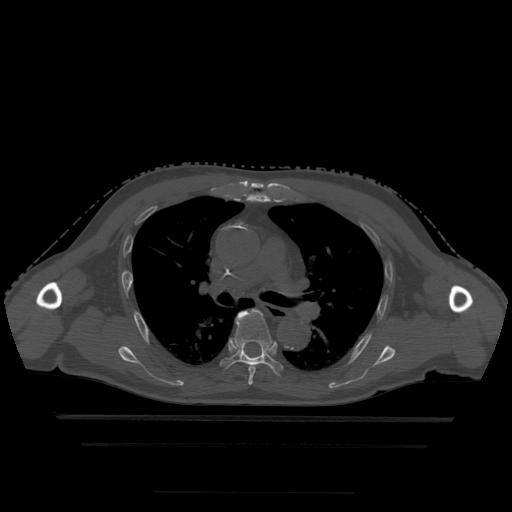
CT including the spine, one axial slice. Position 322 of 522 along the scan axis. Bone window (W 1800 / L 400 HU). 512 × 512 image matrix, field of view 436 × 436 mm. Patient age 68 years. Case-level facts recorded for this patient, not image findings: primary cancer: urothelial.
Structures marked on this image (semi-automatic segmentation, software-assisted and operator-edited):
- T5 vertebra: bounding box <241,316,256,386> (left, top, right, bottom; pixels)
- T6 vertebra: <220,310,284,376>